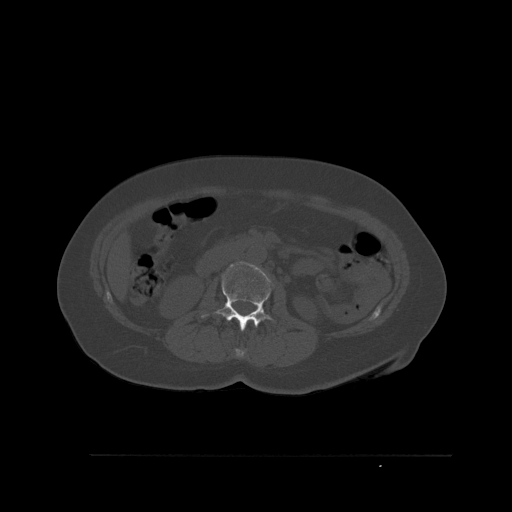
CT including the spine, one axial slice. Bone window (W 1800 / L 400 HU). 1.5 mm slice thickness. 512 × 512 image matrix. Female patient, age 73 years. From the clinical record (not read from this slice): primary cancer: breast; vertebrae with lytic lesions (as recorded): L2.
Annotated regions visible in this slice (semi-automatic segmentation, software-assisted and operator-edited):
- L1 vertebra: bounding box [x1, y1, x2, y2] px = [235, 349, 247, 358]
- L2 vertebra: [201, 261, 275, 331]